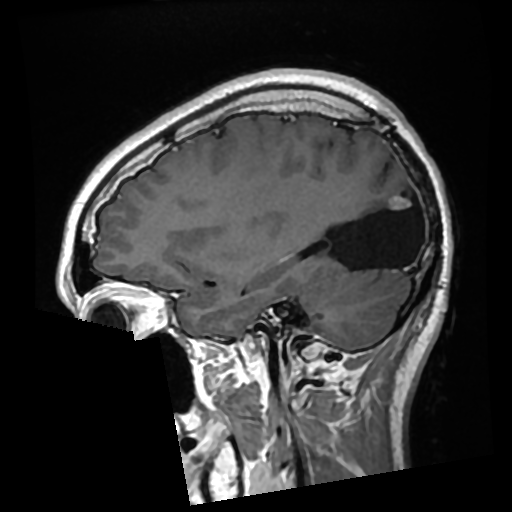
Brain MRI from a brain-tumour surgery series, one sagittal slice; position 95 of 276 along the scan axis; T1-weighted post-contrast; 0.7 mm slice thickness; 512 × 512 image matrix, field of view 250 × 250 mm. From the clinical record (not read from this slice): histopathology: Glioma with ependymal features; WHO grade: 2; tumour location: Left Parietal.
Outlined on this slice (expert manual segmentation):
- previous resection cavity: bounding box (x1, y1, x2, y2) in pixels: (325, 182, 417, 270)
- tumour: (391, 196, 411, 210)